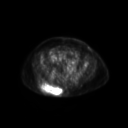
FDG PET of an extremity soft-tissue mass (from a PET/CT study), one axial slice; position 71 of 267 along the scan axis; 3.27 mm slice thickness; 128 × 128 image matrix, field of view 600 × 600 mm. Female patient, age 60 years. From the clinical record (not read from this slice): histological type: spindle cell suggestive of myxofibrosarcoma; grade: intermediate; site of the primary tumour: right buttock.
Outlined on this slice (expert contour drawn on MRI and transferred to this co-registered scan by the dataset authors):
- gross tumour volume (mass): bounding box <38,82,63,96> (left, top, right, bottom; pixels)